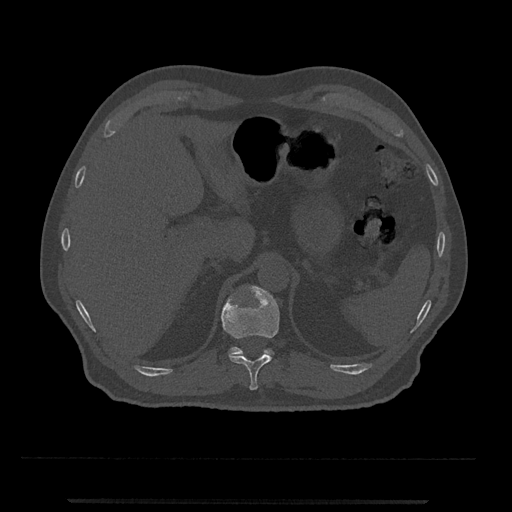
CT including the spine, one axial slice; position 446 of 797 along the scan axis; bone window (W 1800 / L 400 HU); 0.5 mm slice thickness; 512 × 512 image matrix, field of view 419 × 419 mm. Male patient, age 63 years. From the clinical record (not read from this slice): primary cancer: prostate.
Outlined on this slice (semi-automatic segmentation, software-assisted and operator-edited):
- T11 vertebra: bounding box (x1, y1, x2, y2) in pixels: (221, 286, 280, 390)
- T12 vertebra: (228, 347, 274, 356)